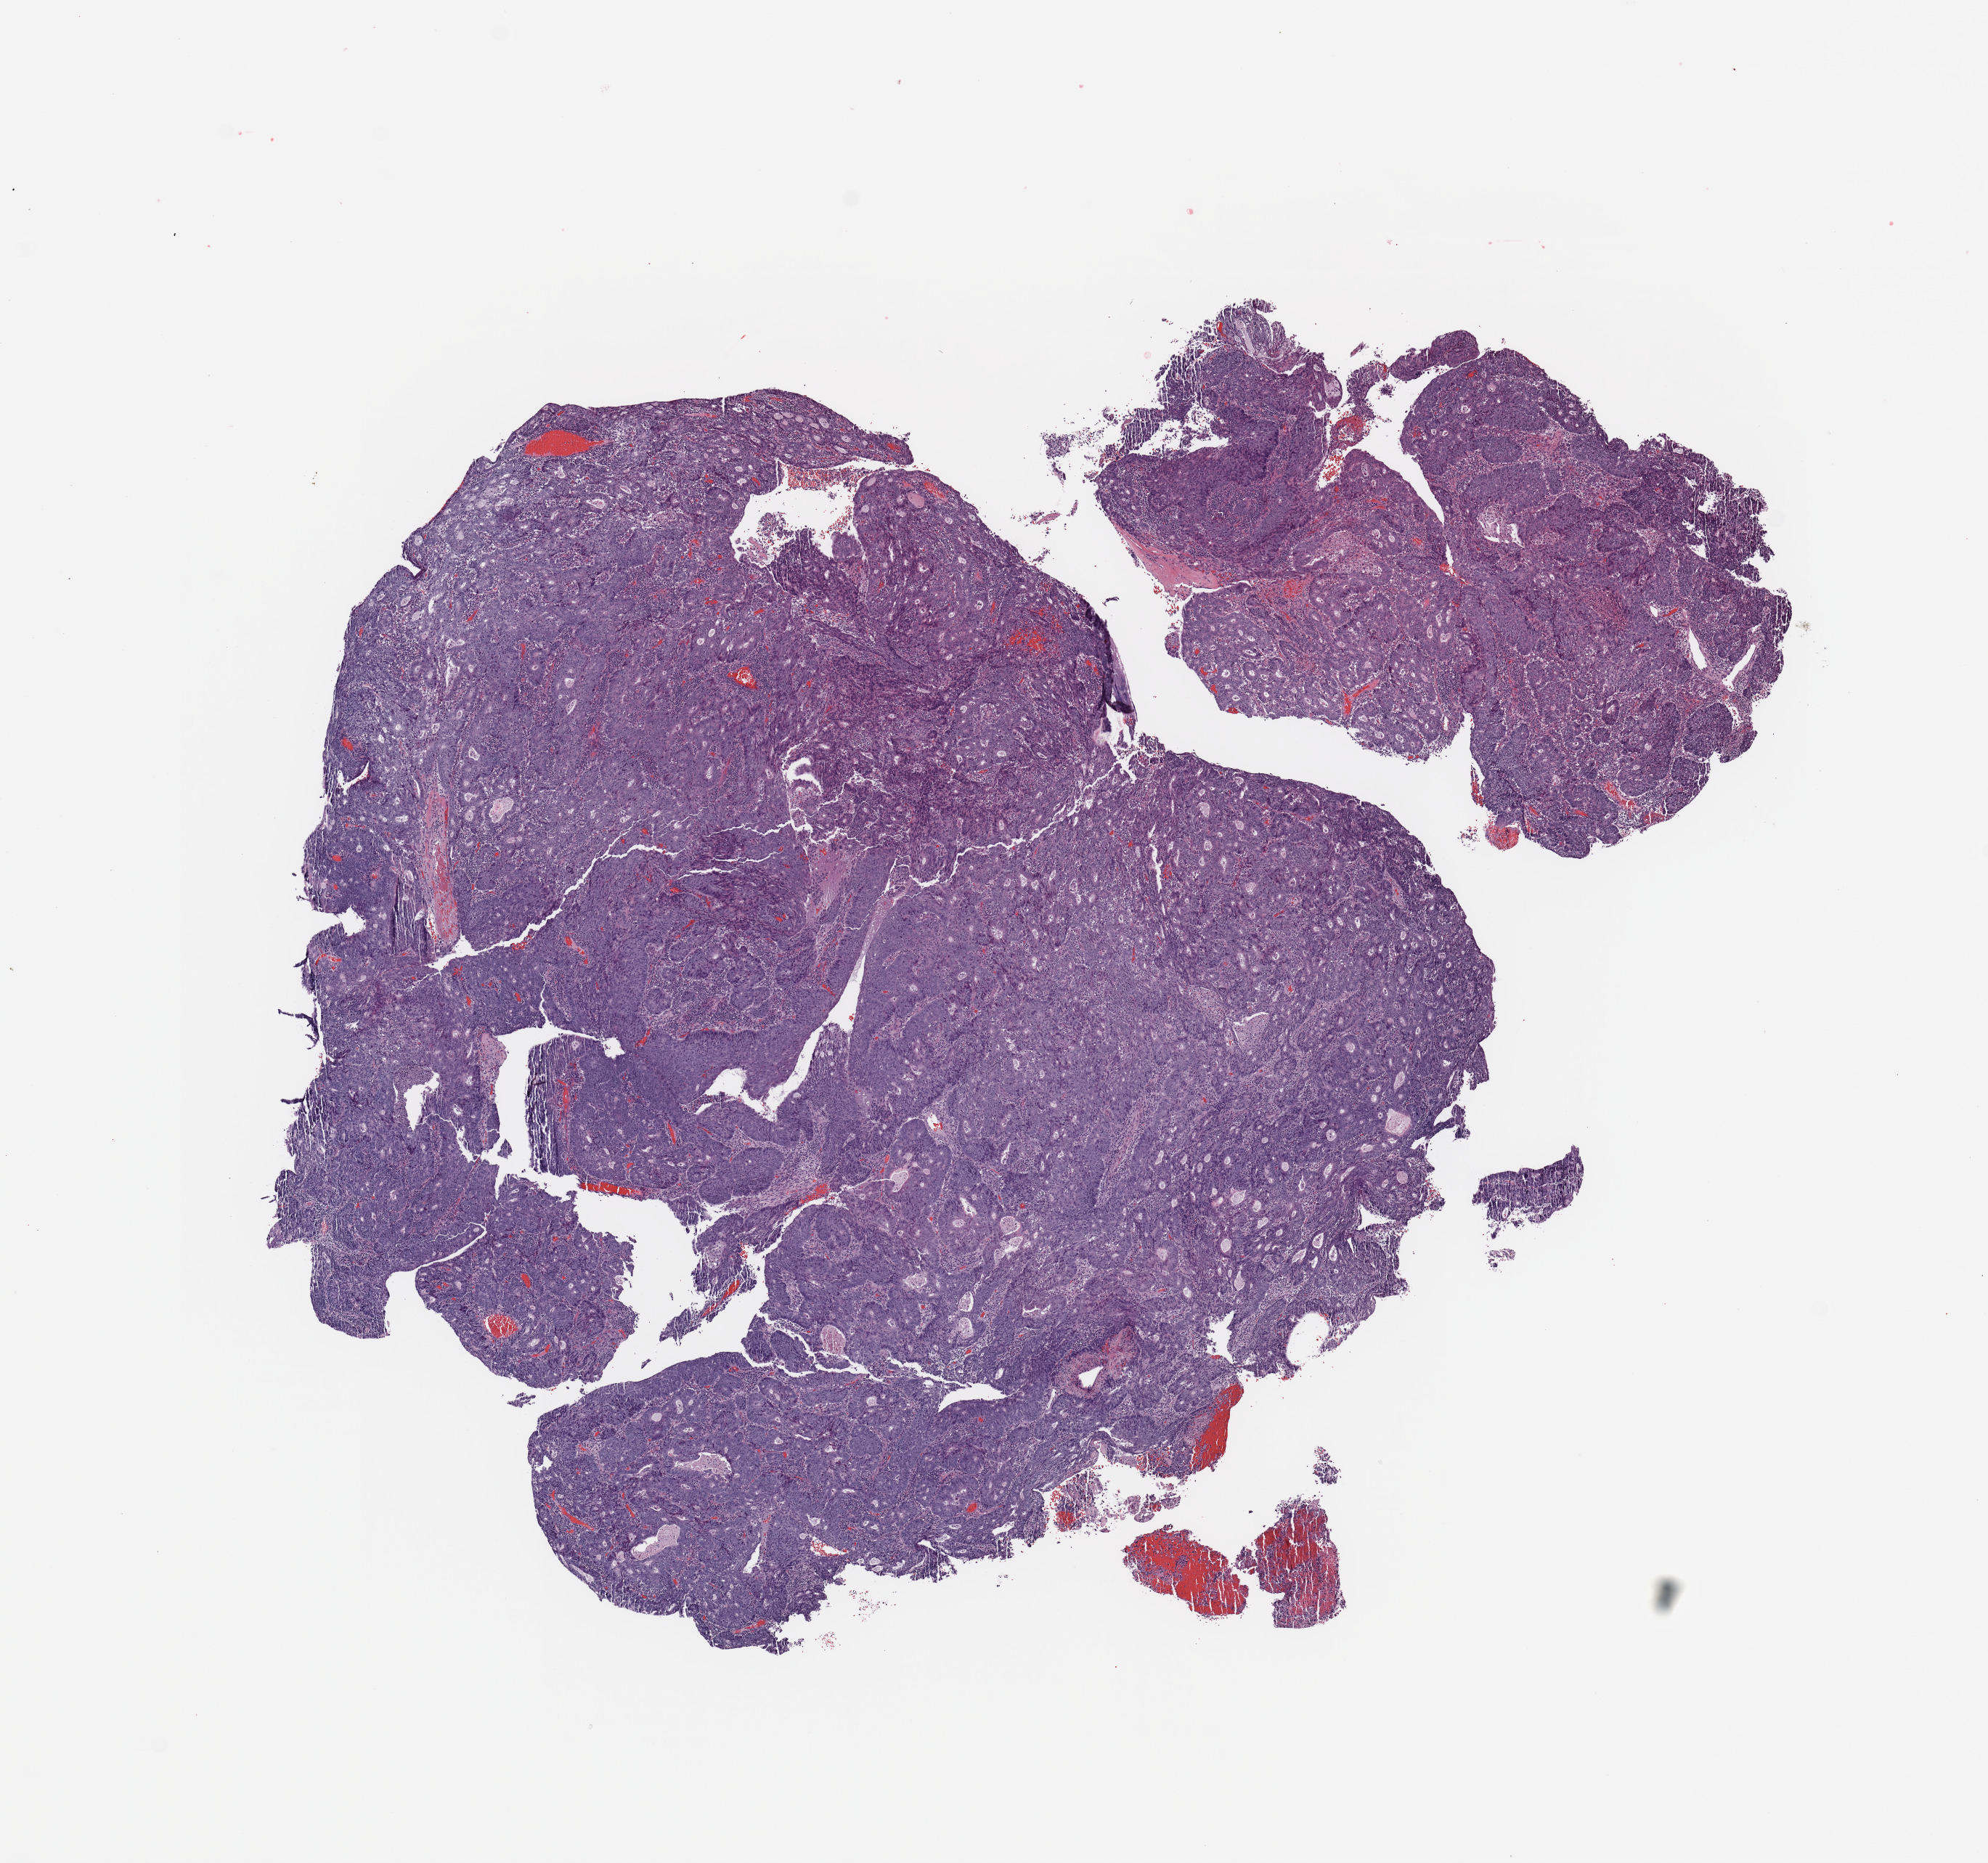
Digitized Hematoxylin and eosin (H&E) stained tissue section (whole slide), shown as a low-resolution overview of the whole scanned area (about 10.8 x 10.1 mm, slide scanned at 20x); tumour tissue sample, sampled site: uterus. Female, 71 y/o. Histologic grade: G3 (poorly differentiated). Pathologist review of this section (percent, as recorded): tumour nuclei 85%, necrosis 2%.
Histologic diagnosis: Endometrioid adenocarcinoma, NOS. AJCC pathologic stage: I.